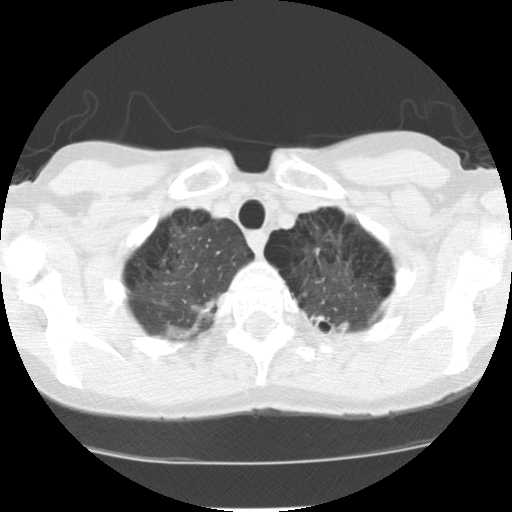
Low-dose screening chest CT, one axial slice; slice 103 of 116 in the series (ordered by position); 120 kVp; lung window (W 1500 / L -600 HU); 2.5 mm slice thickness; 512 × 512 image matrix.
Structures marked on this image (expert manual segmentation):
- lesion 1 (tumor, upper lobe of left lung): bounding box <310,315,349,332> (left, top, right, bottom; pixels)